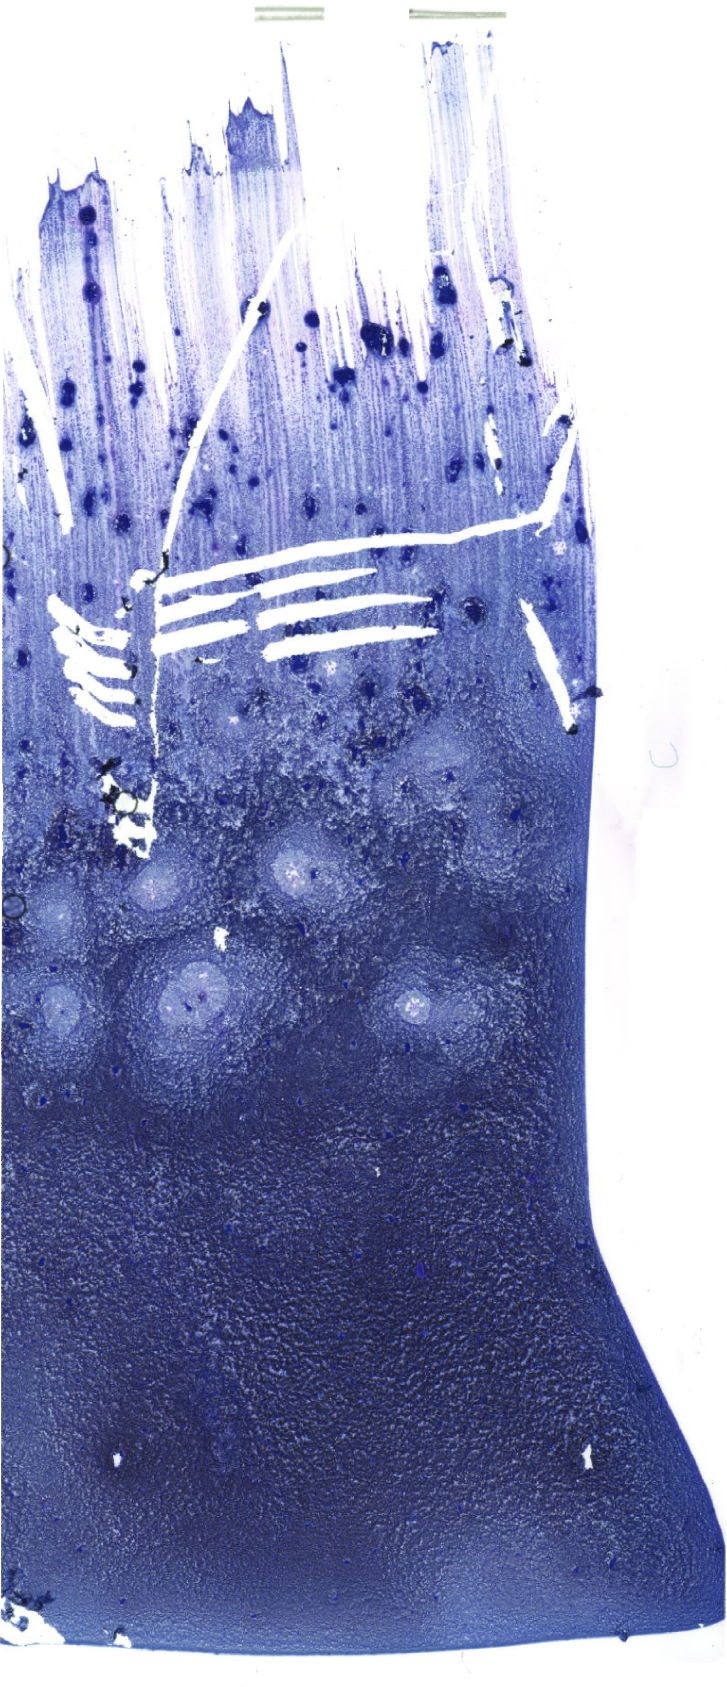
Bone marrow aspirate smear, May-Grünwald-Giemsa (MGG) stain, whole-slide image, shown as a low-resolution overview of the whole scanned area (about 20.6 x 47.8 mm). Patient sex: male.
Diagnosis: Acute Myeloid Leukemia with Maturation.